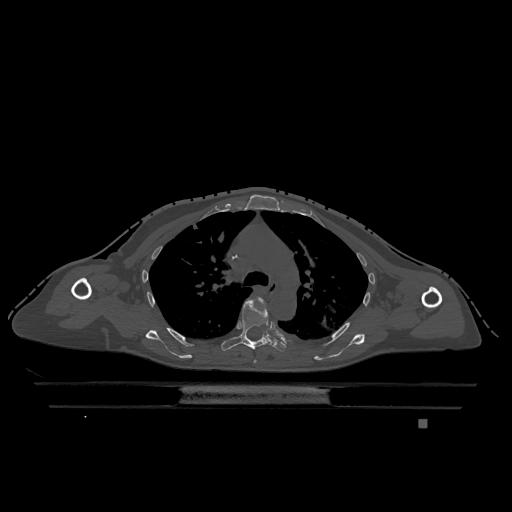
CT including the spine, one axial slice. Position 846 of 1317 along the scan axis. Bone window (W 1800 / L 400 HU). 0.5 mm slice thickness. 512 × 512 image matrix. Female patient, age 74 years. Case-level facts recorded for this patient, not image findings: primary cancer: lung; vertebrae with lytic lesions (as recorded): T1, T4, T5, T6, L4, L5.
Annotated regions visible in this slice (semi-automatically segmented with operator editing):
- T4 vertebra: bounding box <254,298,267,363> (left, top, right, bottom; pixels)
- T5 vertebra: <221,299,287,353>